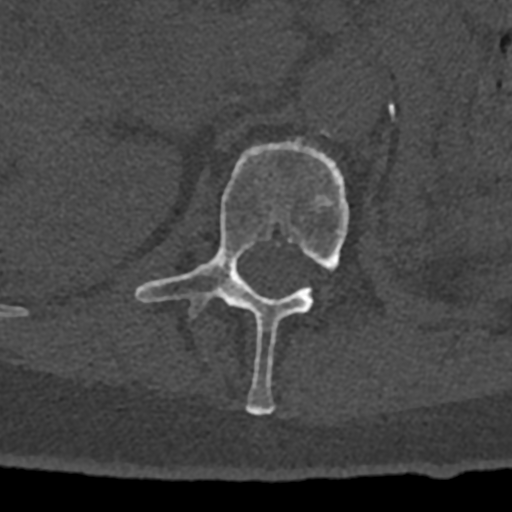
CT including the spine, one axial slice; slice 431 of 797 in the series (ordered by position); reconstruction kernel Br40s/3; bone window (W 1800 / L 400 HU); 0.5 mm slice thickness; 512 × 512 image matrix. Patient: male, 74 years. From the clinical record (not read from this slice): primary cancer: renal.
Structures marked on this image (semi-automatic segmentation, software-assisted and operator-edited):
- L1 vertebra: bounding box [x1, y1, x2, y2] px = [135, 139, 349, 415]